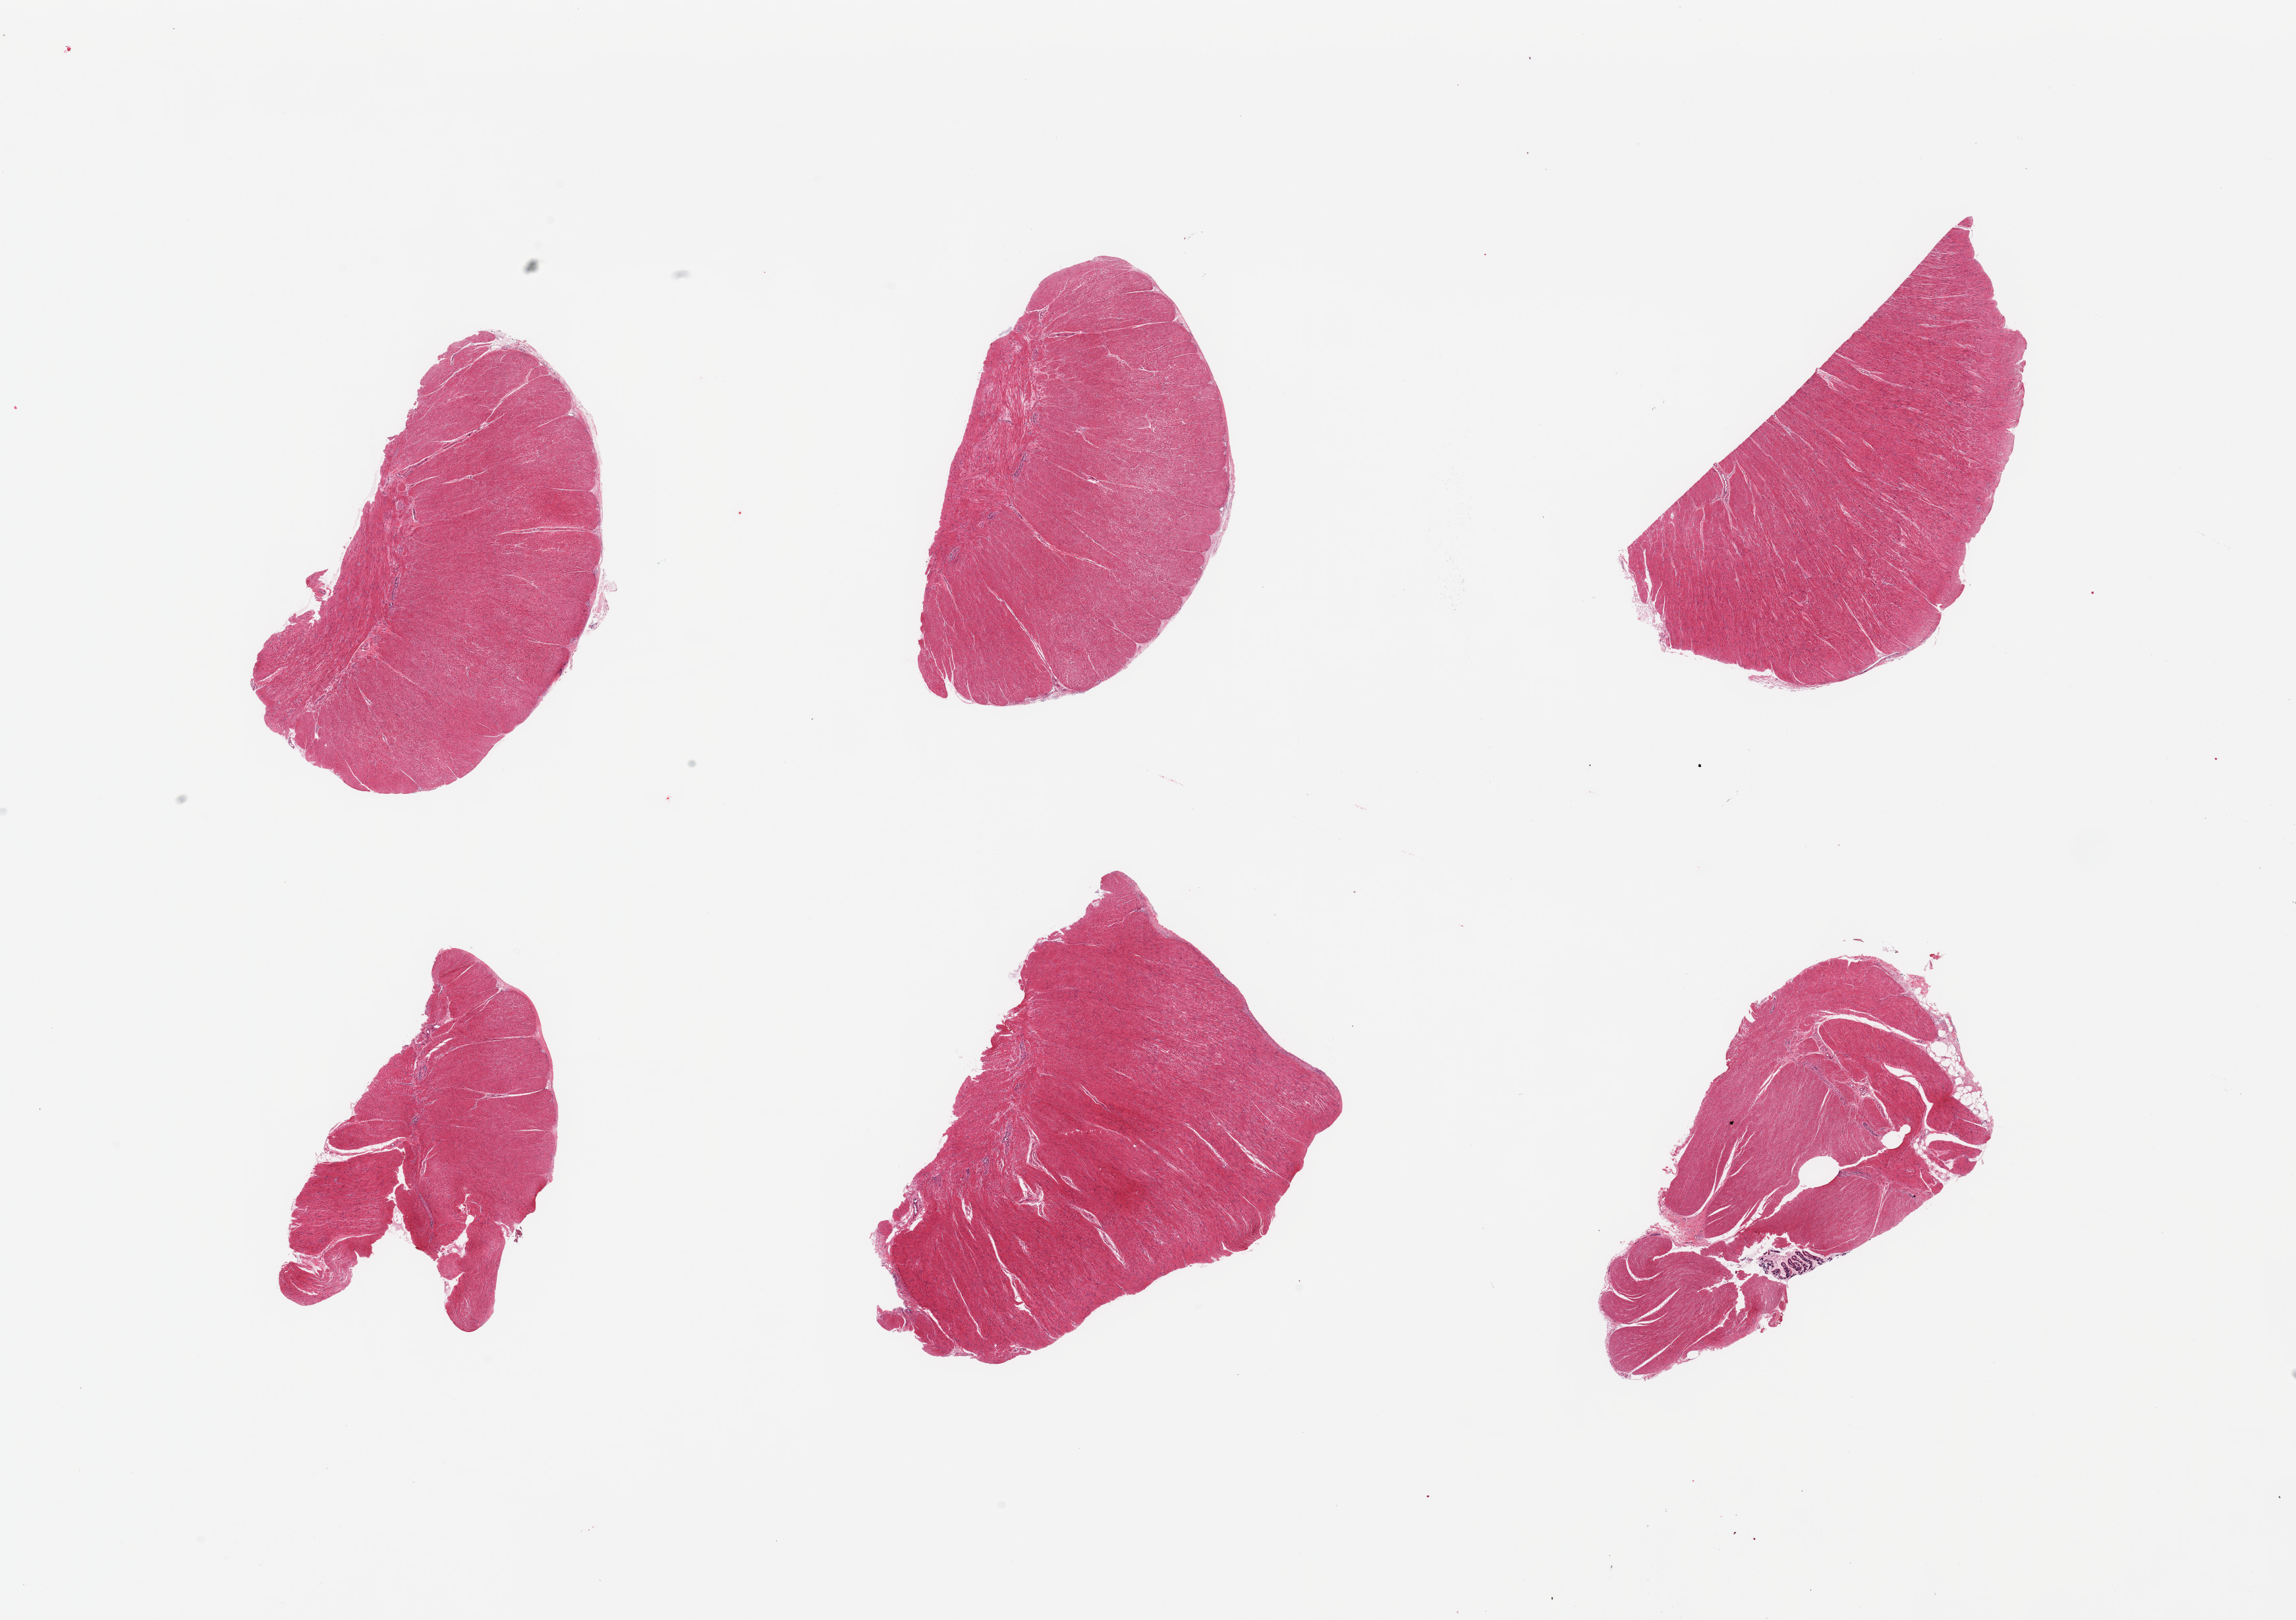
Whole-slide image, haematoxylin and eosin stain, shown as a low-resolution overview of the whole scanned area (about 27.6 x 19.4 mm, slide scanned at 20x). PAXgene-fixed paraffin-embedded (PFPE) section. Sampled site (target tissue): sigmoid colon. Tissue donor sample. Male donor.
Reviewer comment on this tissue sample: 6 pieces; well dissected muscle; a 0.7mm mucosal contaminant (carry-over) labeled.